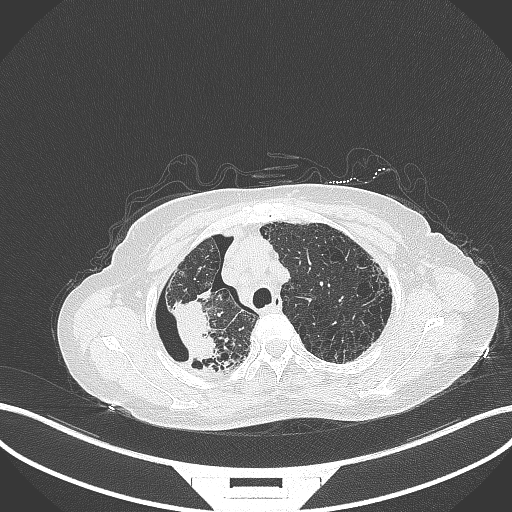
Chest CT, one axial slice. Position 284 of 408 along the scan axis. Lung window (W 1500 / L -600 HU). 1 mm slice thickness. 512 × 512 image matrix, field of view 400 × 400 mm. Patient: female, 64 years. From the clinical record (not read from this slice): clinical TNM (as recorded): T3 N3 M0.
Structures marked on this image (rectangle marked by the reading radiologist):
- lung tumour (recorded histology: squamous cell carcinoma): bounding box <164,288,225,359> (left, top, right, bottom; pixels)